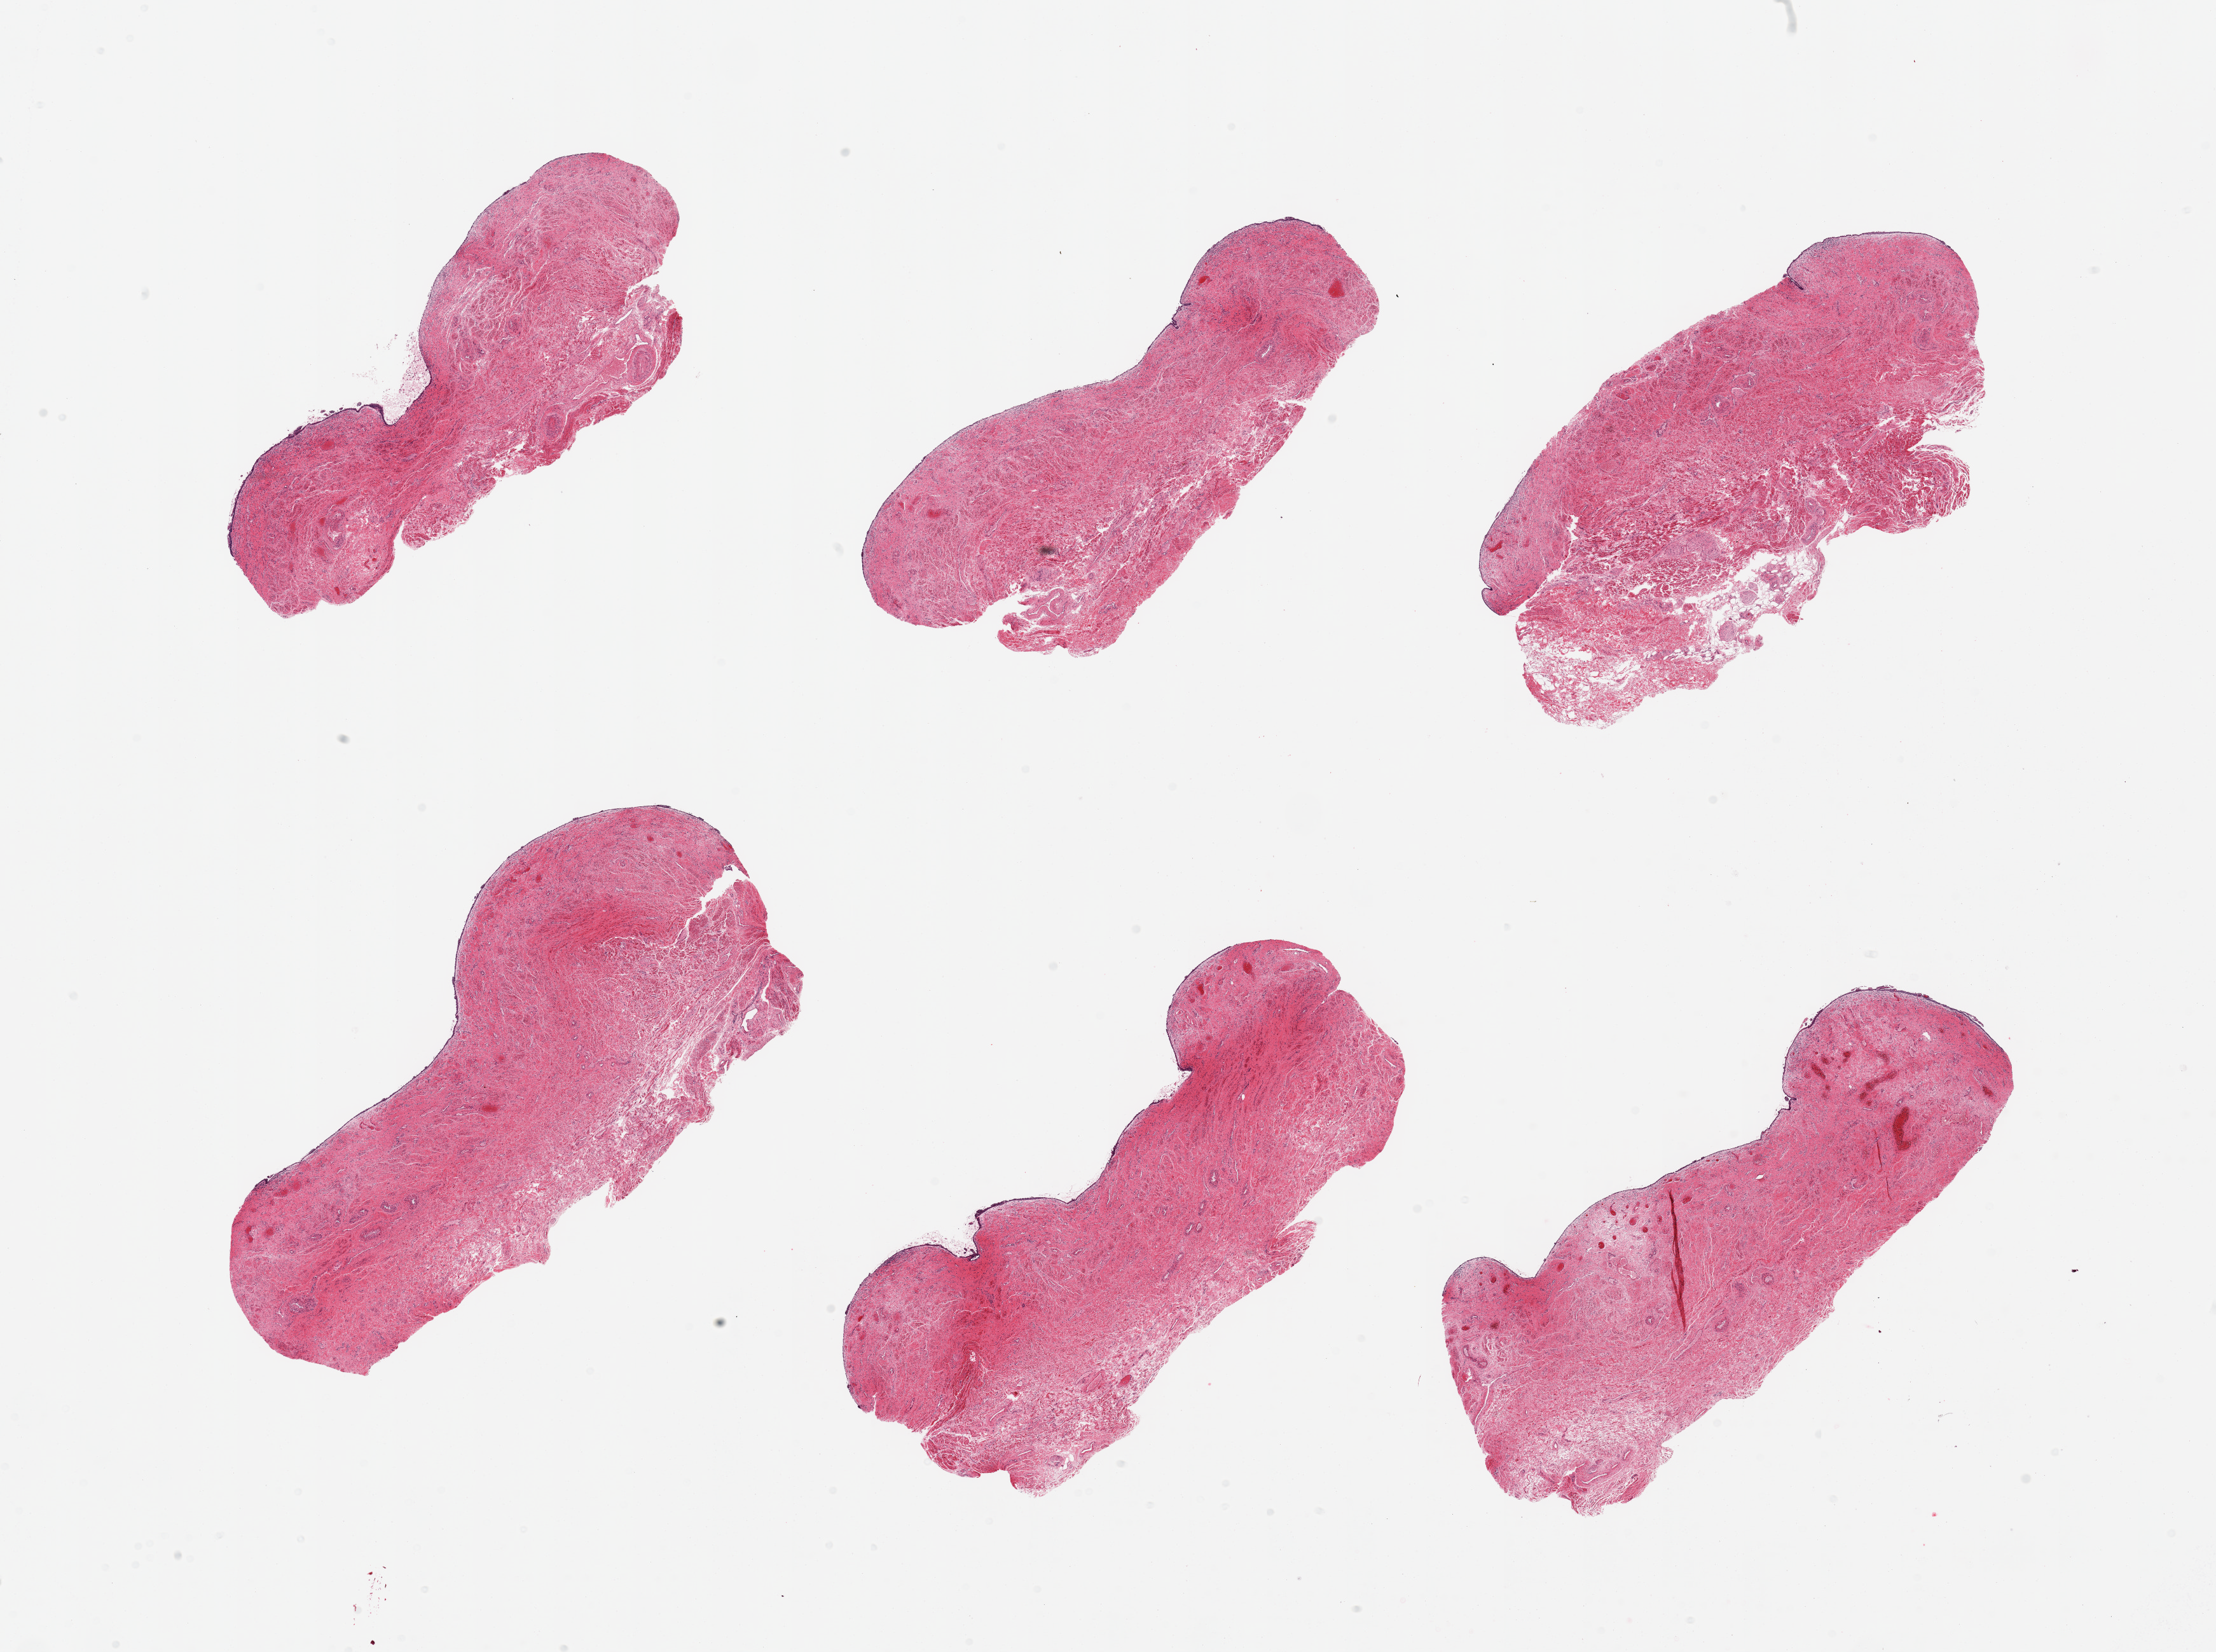
Haematoxylin and eosin whole-slide image — whole scanned area (about 27.6 x 20.5 mm, acquisition: 20x scan) shown as a low-resolution overview; PAXgene-fixed paraffin-embedded (PFPE) section; target tissue: vagina; tissue donor sample. Donor: female.
Reviewer comment on this tissue sample: 6 pieces; largely sloughed atrophic surface.